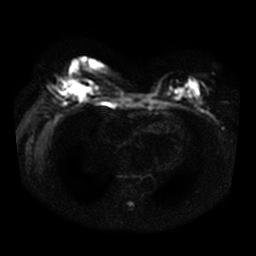
Breast MRI, one axial slice; slice 18 of 34 in the series (ordered by position); diffusion-weighted series; image 2 of 4 stored at this slice position (different b-values; order by instance number); 3 T; 256 × 256 image matrix. Female patient.
Annotated regions visible in this slice (outlined manually by an expert reader):
- tumour on diffusion-weighted imaging: box from (x=65, y=81) to (x=86, y=97) px